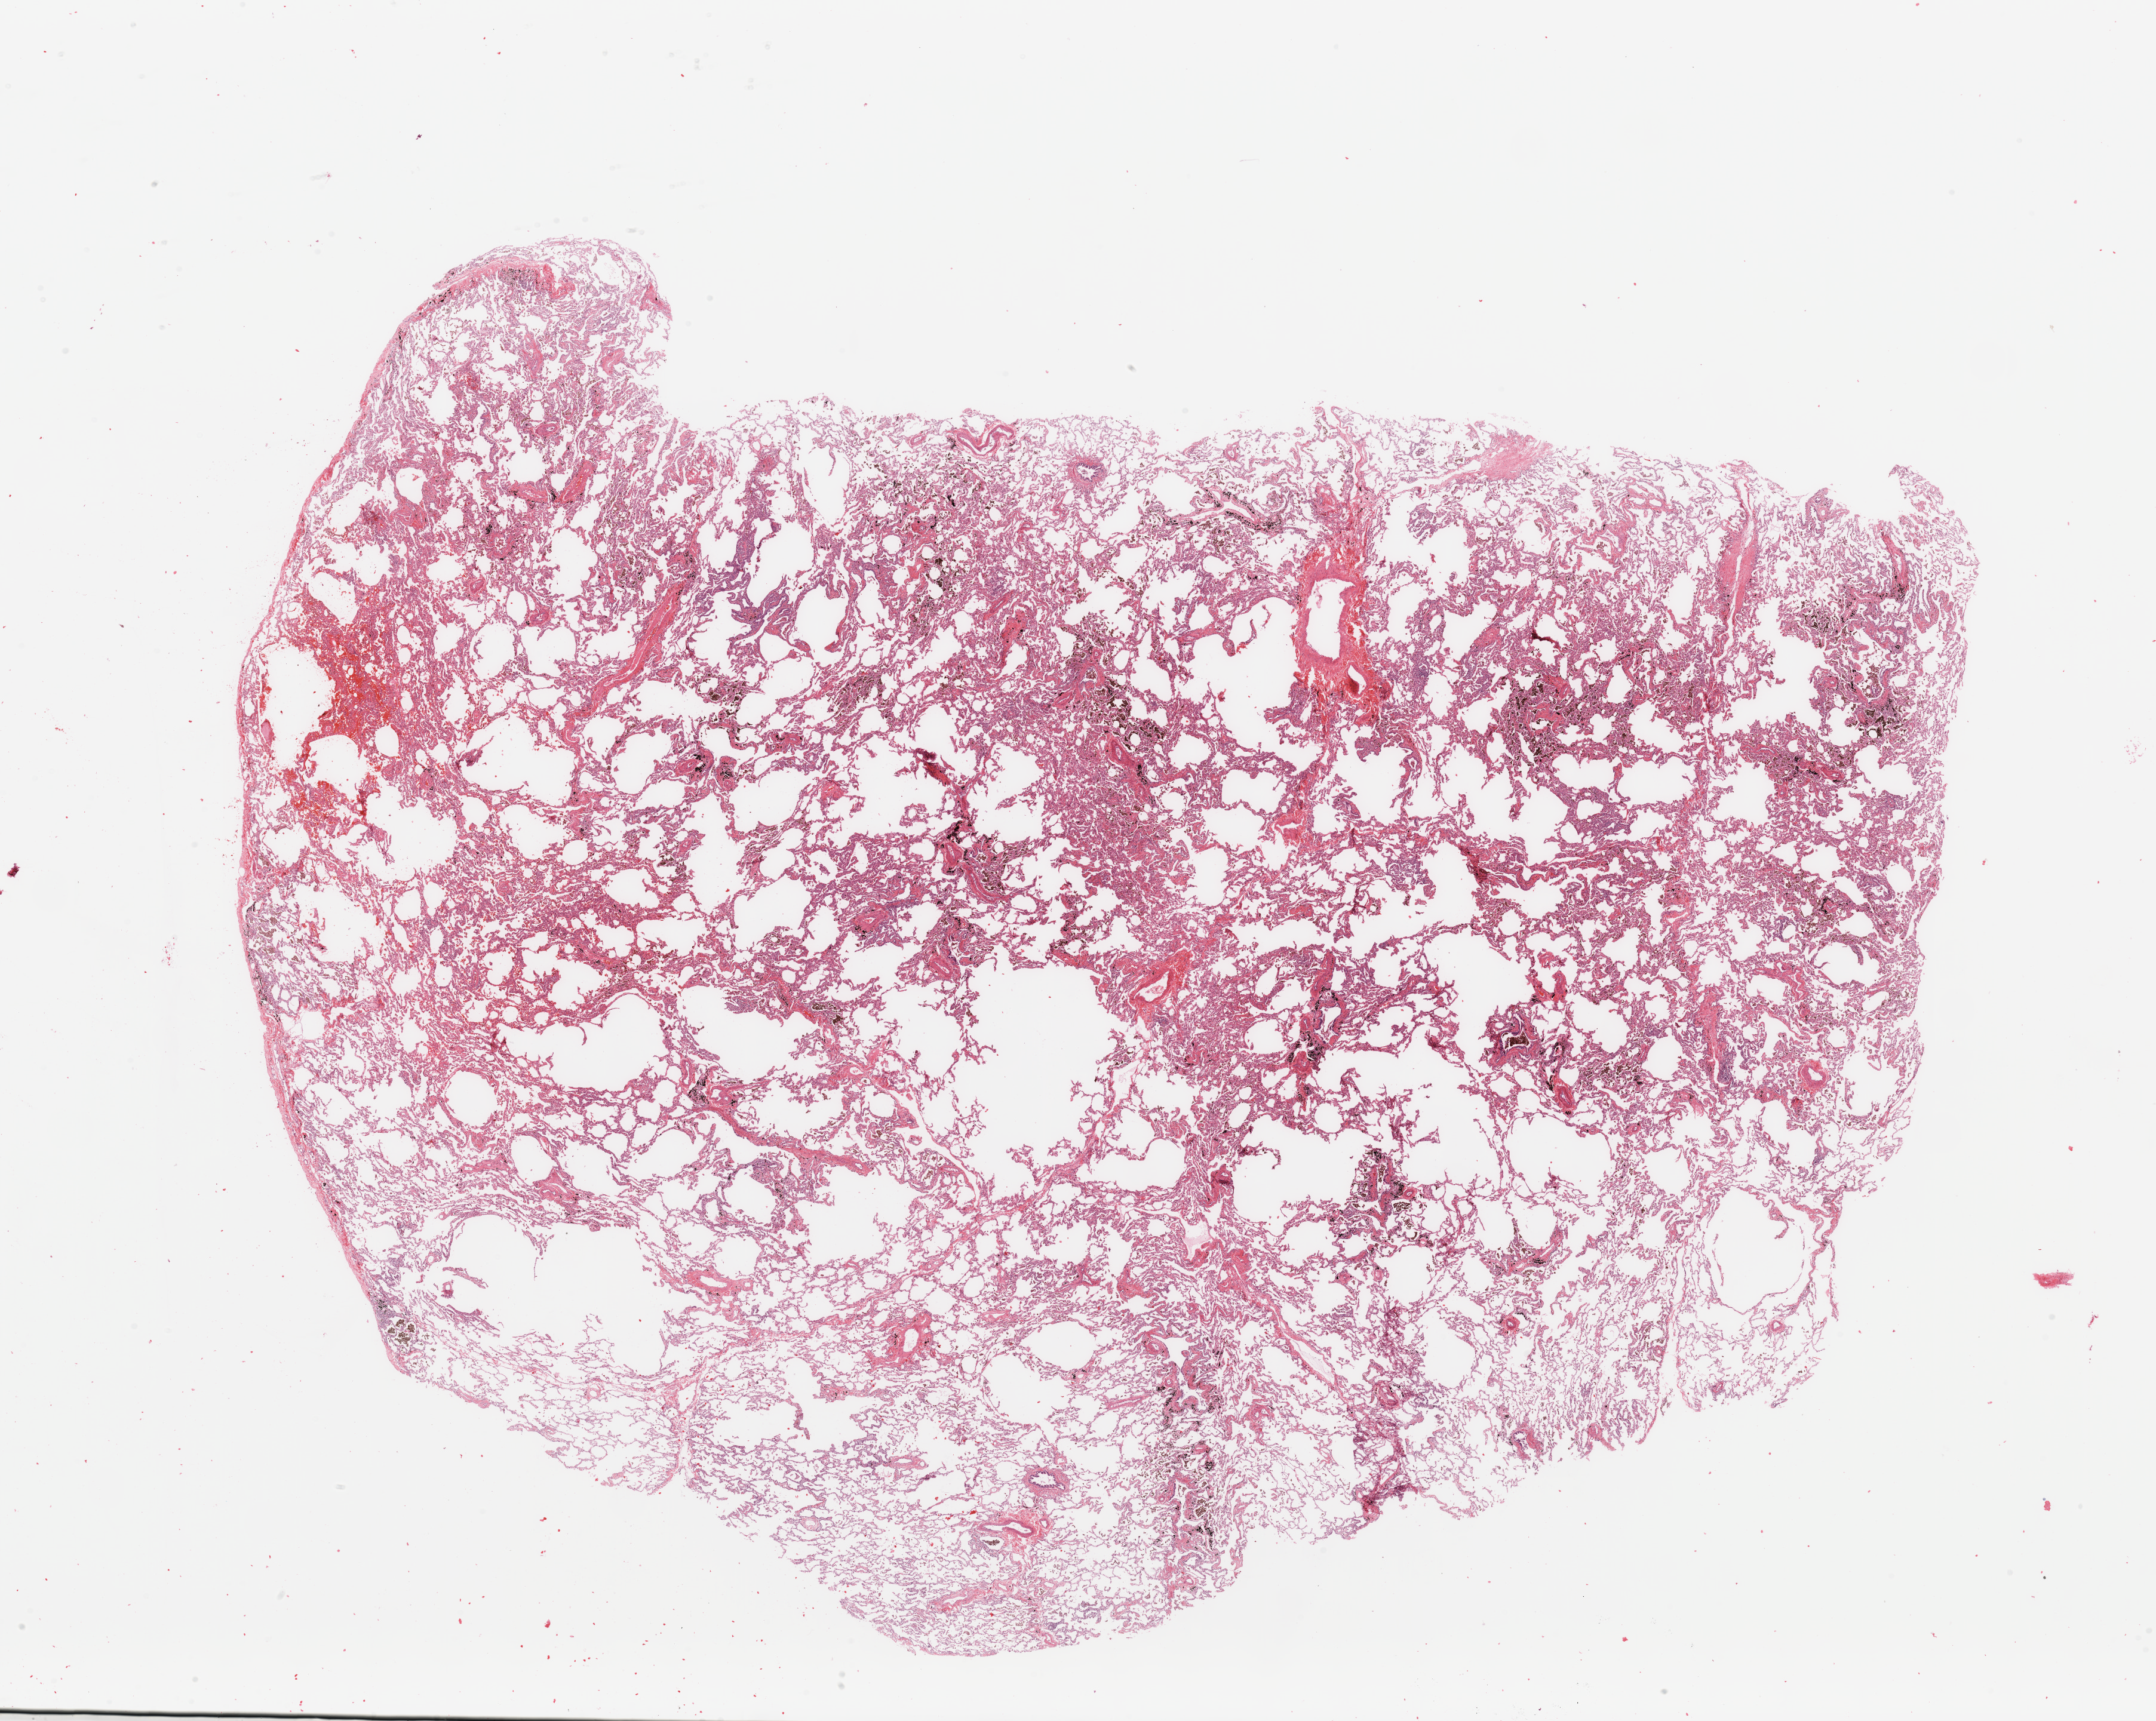
Digitized H&E-stained tissue section (whole slide), a low-resolution overview of the entire scanned area, about 28.5 x 22.8 mm. Normal (non-tumour) tissue sample, lung. Male, 49 y/o.
This section: normal (non-tumour) tissue from the same patient. Patient diagnosis: Adenocarcinoma, NOS.